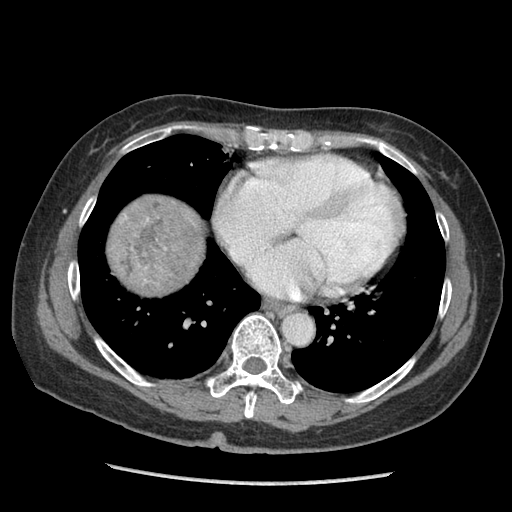
Contrast-enhanced abdominal CT (liver protocol), one axial slice; slice 95 of 105 in the series (ordered by position); reconstruction kernel STANDARD; 140 kVp; soft-tissue window (W 400 / L 40 HU); 2.5 mm slice thickness; 512 × 512 image matrix, field of view 340 × 340 mm. From the clinical record (not read from this slice): diagnosis: hepatocellular carcinoma (patient treated with transarterial chemoembolisation; whether this scan precedes or follows treatment is not stated here); TNM stage (as recorded): Stage-I; Child-Pugh class: A; tumour differentiation: moderately differentiated; tumour nodularity: uninodular.
Structures marked on this image (semi-automatically segmented with operator editing):
- liver parenchyma outside the tumour (the mass and vessels are separate outlines, so this box may not span the whole liver): box from (x=108, y=194) to (x=204, y=294) px
- mass: (x=111, y=198)–(x=200, y=293)